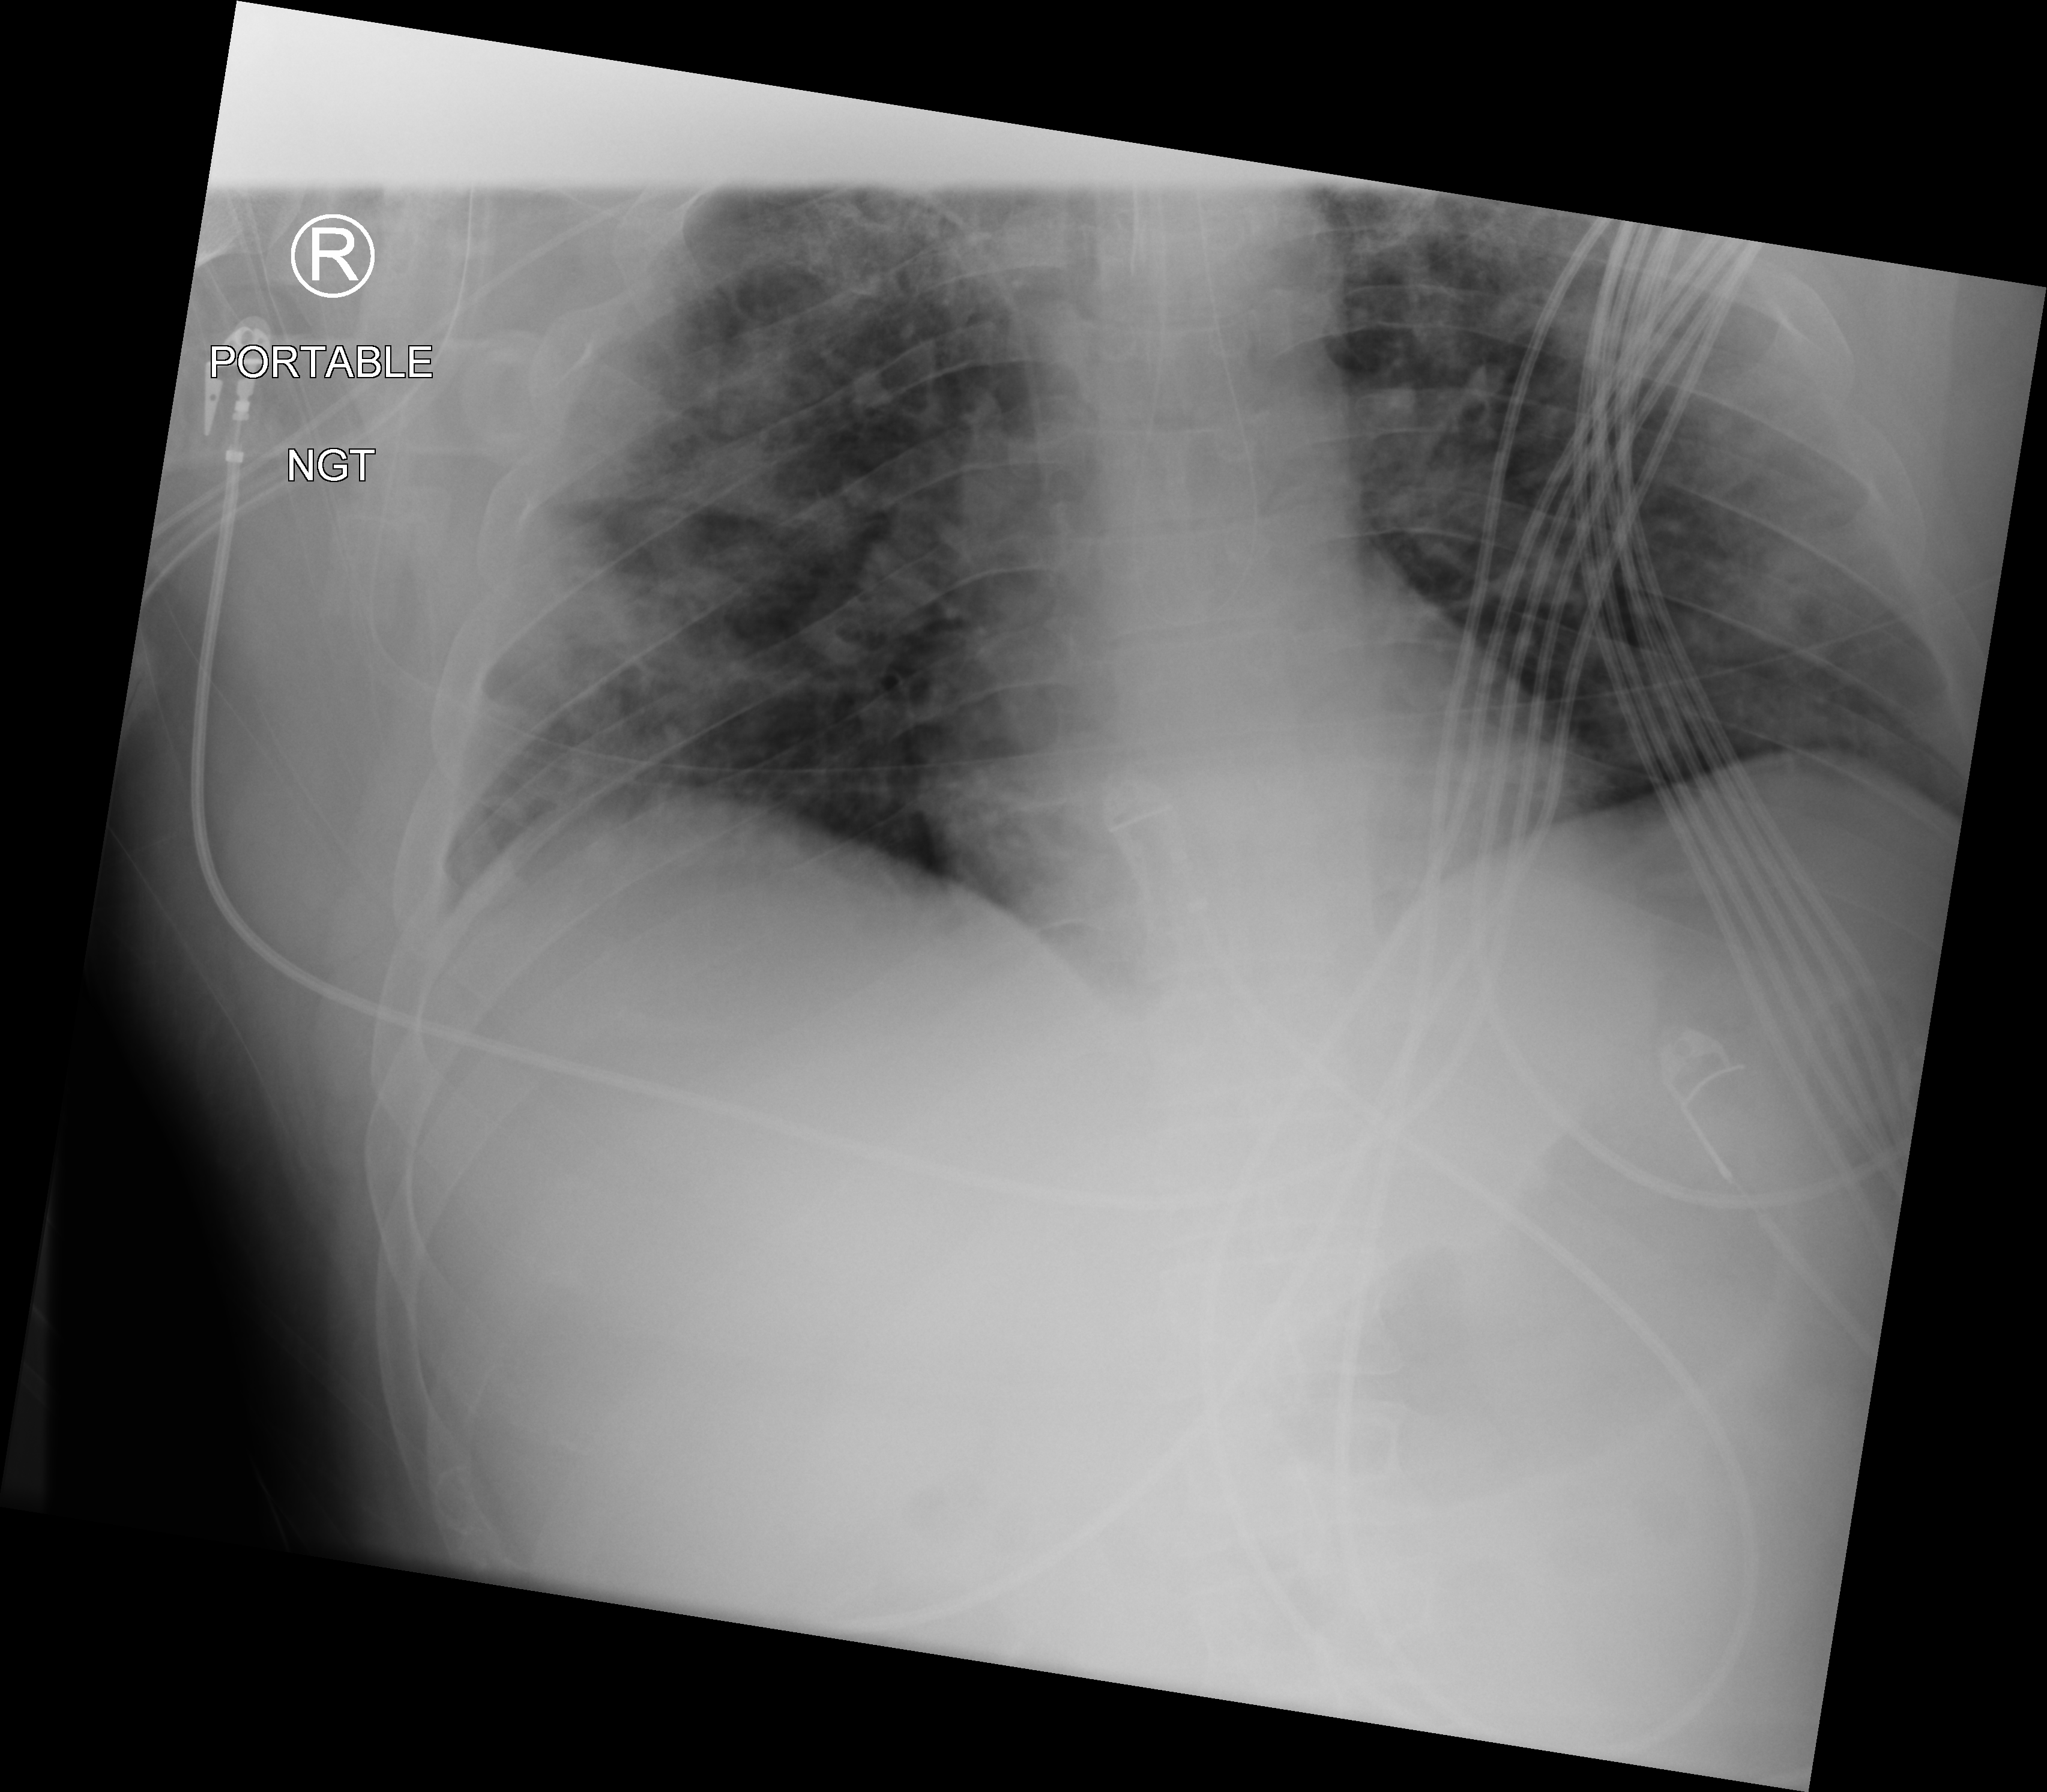
Chest X-ray (portable); anteroposterior (AP) projection. Patient hospitalised with COVID-19; female, aged 18–59 years.
Admission-level facts for this patient (not findings on this image; timing relative to this image not recorded):
- length of hospital stay: 16 days